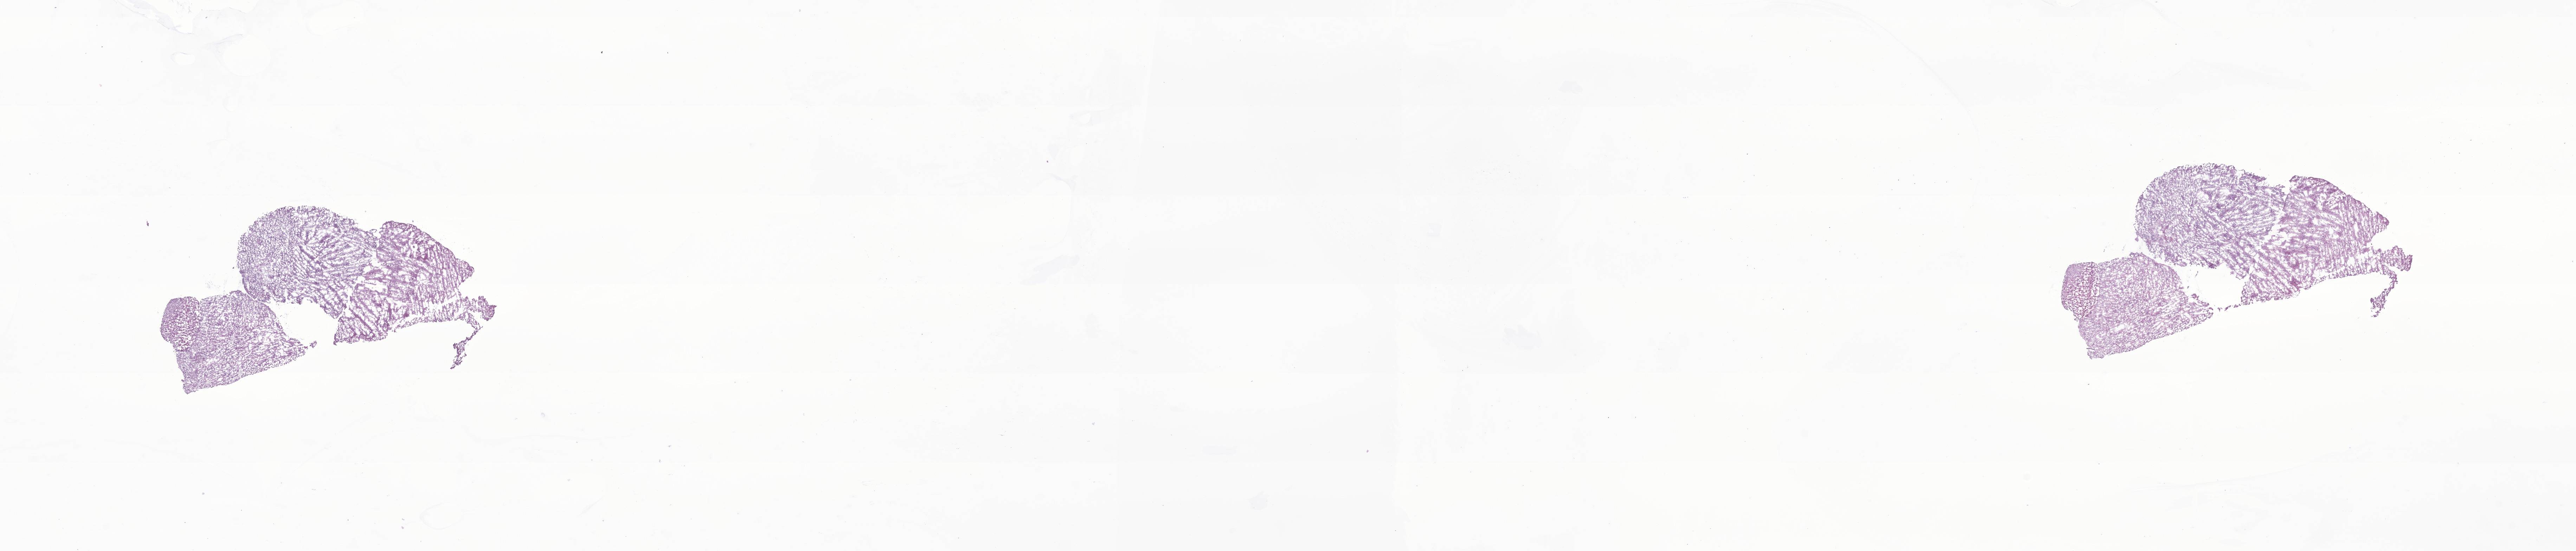
Whole-slide image, hematoxylin and eosin (H&E) stain of tumor tissue from the brain — low-resolution overview of the scanned area, about 30.9 x 6.6 mm, frozen section (OCT-embedded). Patient female; age 611 days (about 1.7 years).
Diagnosis (ICD-O-3 morphology term): Neoplasm, uncertain whether benign or malignant.